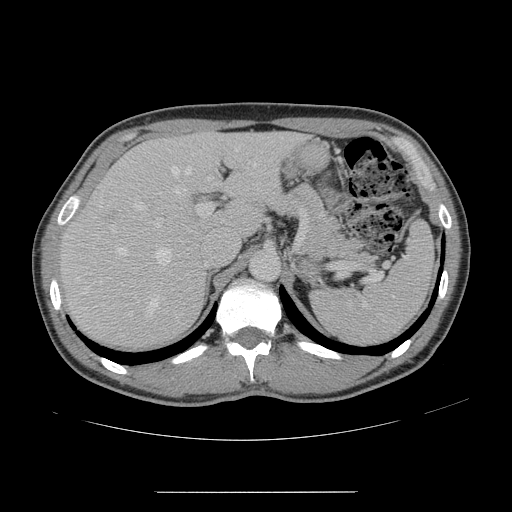
Contrast-enhanced abdominal CT, one axial slice; slice 102 of 178 in the series (ordered by position); intravenous contrast given; soft-tissue window (W 400 / L 40 HU); 2.5 mm slice thickness; 512 × 512 image matrix. Male patient, age 53 years. Case-level facts recorded for this patient, not image findings: diagnosis: colorectal cancer liver metastases, imaged before liver resection; multiple liver metastases: yes; largest metastasis: 2.4 cm; disease in both lobes: no.
Outlined on this slice (manually delineated by an expert):
- hepatic veins: bounding box (x1, y1, x2, y2) in pixels: (117, 147, 256, 315)
- liver: (62, 134, 301, 347)
- planned liver remnant (the part of the liver to remain after resection): (148, 135, 300, 233)
- portal vein (with intrahepatic branches): (132, 200, 213, 229)
- liver metastasis: (108, 212, 116, 221)